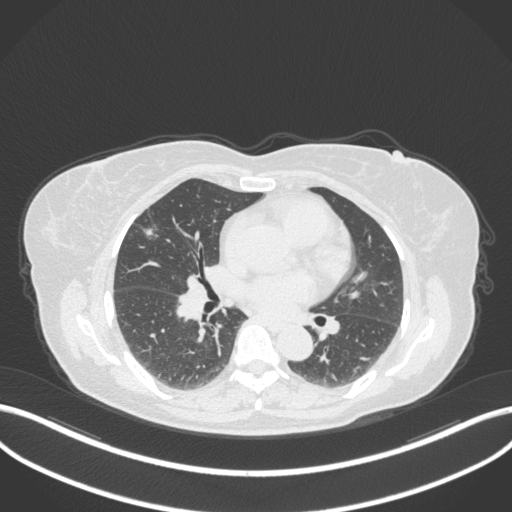
Chest CT, one axial slice. Position 171 of 310 along the scan axis. Reconstruction kernel B31f. 120 kVp. Lung window (W 1500 / L -600 HU). 1 mm slice thickness. 512 × 512 image matrix, field of view 400 × 400 mm. Patient: female, 55 years. From the clinical record (not read from this slice): clinical TNM (as recorded): T1b N0 M0; histopathological grade: G2.
Annotated regions visible in this slice (bounding box drawn by a radiologist):
- lung tumour (recorded histology: adenocarcinoma): box from (x=139, y=222) to (x=158, y=240) px